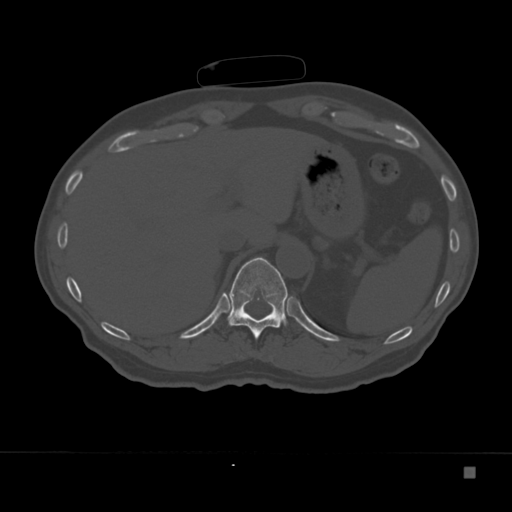
CT including the spine, one axial slice; position 153 of 332 along the scan axis; reconstruction kernel Br40s; 120 kVp; bone window (W 1800 / L 400 HU); 1.5 mm slice thickness; 512 × 512 image matrix, field of view 389 × 389 mm. Patient: male, 72 years. From the clinical record (not read from this slice): primary cancer: skeletal.
Structures marked on this image (semi-automatic segmentation, software-assisted and operator-edited):
- T11 vertebra: bounding box <227,257,288,339> (left, top, right, bottom; pixels)